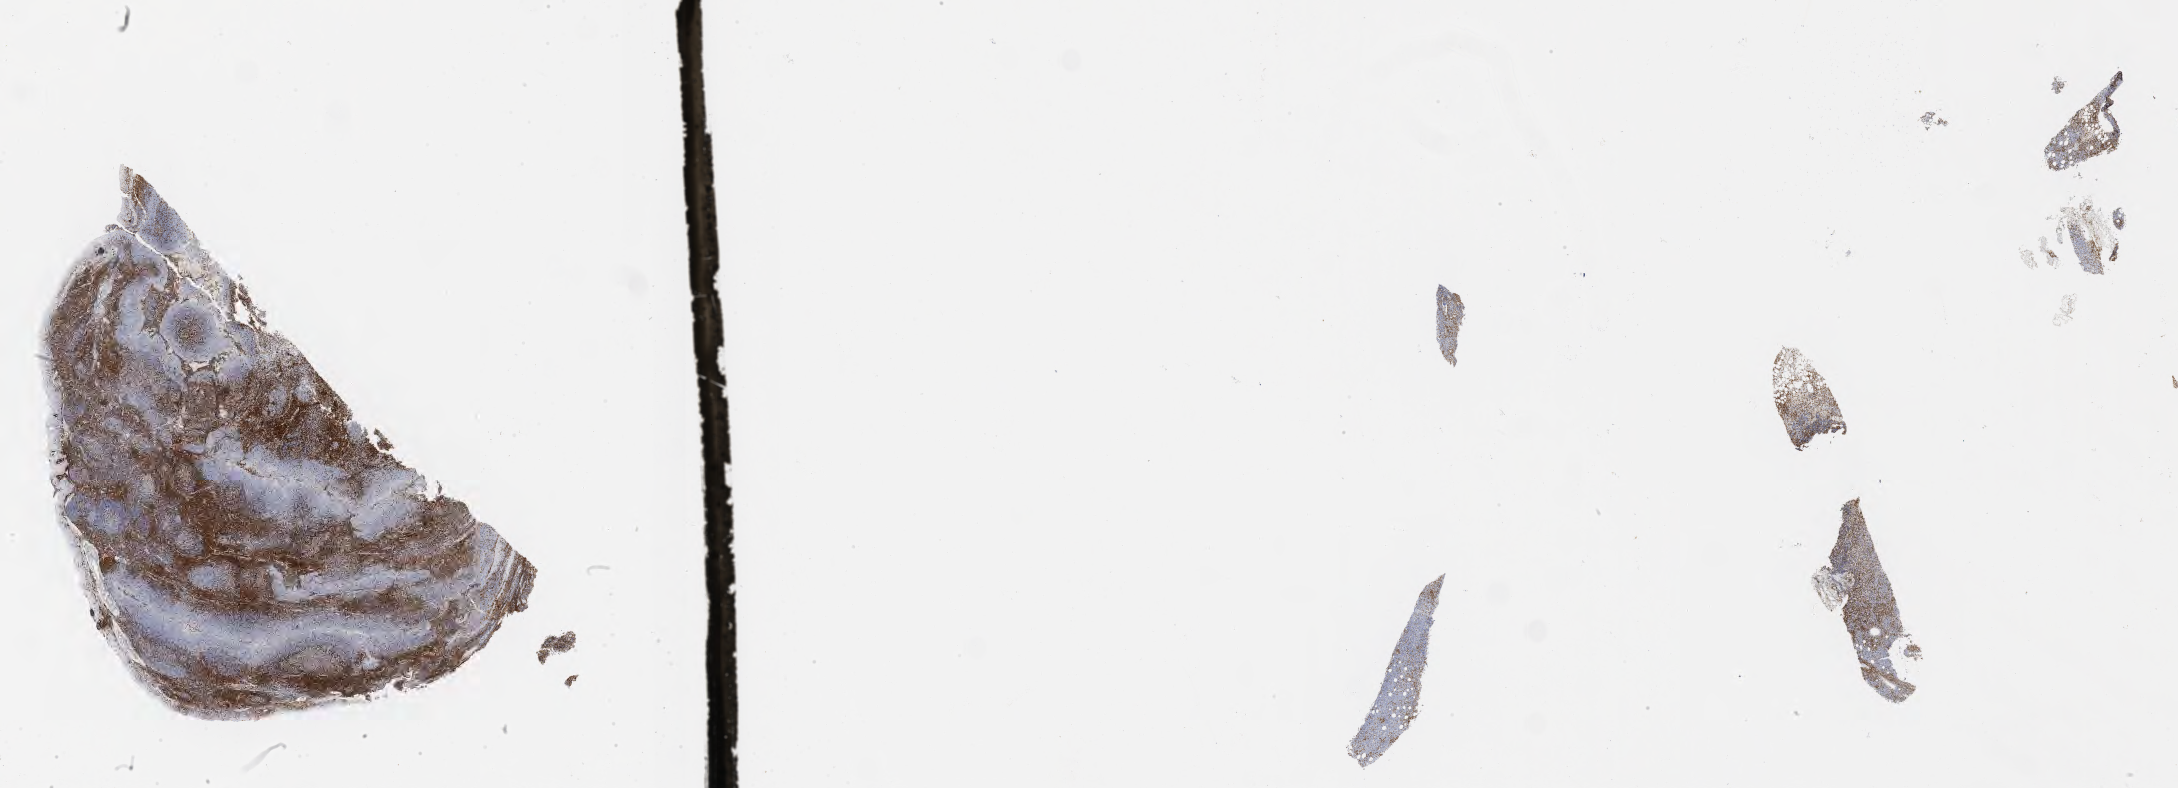
Whole-slide image, immunohistochemical stain for CD3, low-resolution overview of the scanned area, about 35.2 x 12.7 mm, specimen: tumor tissue. Patient male; 33 years old.
Diagnosis: Burkitt lymphoma, NOS.